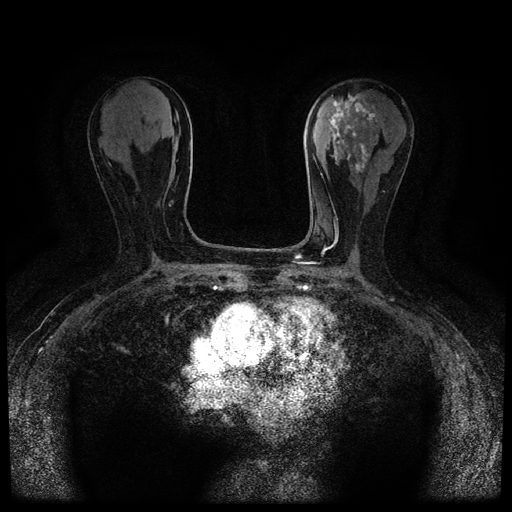
Breast MRI (dynamic contrast-enhanced, multi-phase), one axial slice. Slice 39 of 116 in the series (ordered by position). Dynamic contrast-enhanced series, time point 2 of 5 at this slice position (early post-contrast). 1.5 T. TE 2.7 ms, TR 5.4 ms. 2 mm slice thickness. 512 × 512 image matrix, field of view 320 × 320 mm. Female patient, age 80 years.
Outlined on this slice (semi-automatic segmentation, software-assisted and operator-edited):
- breast lesion (labelled 'tumour' in the annotation; benign lesions carry a separate 'benign' label): bounding box [x1, y1, x2, y2] px = [327, 94, 379, 173]